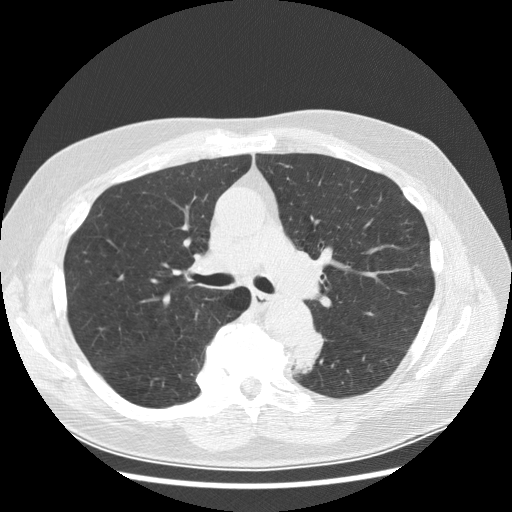
Low-dose screening chest CT, axial slice, baseline screening round, lung window (W 1500 / L -600 HU), 2.5 mm slice thickness, 512 × 512 image matrix. Male, age 70 years at enrolment.
- Expert reader's lesion annotation, bounding box <278,331,329,382> (left, top, right, bottom; pixels).
- Reader record for this screening exam (exam-level; its link to the box is not recorded): non-calcified nodule or mass ≥4 mm, left lower lobe, 27 × 16 mm, spiculated (stellate) margins, soft tissue attenuation, pre-existing on the prior screen: yes; interval growth: yes.
- Official screen result: positive, change unspecified: nodule(s) >= 4 mm or enlarging nodule(s), mass(es), or other non-specific abnormalities suspicious for lung cancer.
- Participant outcome: lung cancer diagnosed 97 days after this screen — papillary adenocarcinoma, NOS, left lower lobe, moderately differentiated (G2), stage IB (AJCC 6th edition), 35 mm at pathology.